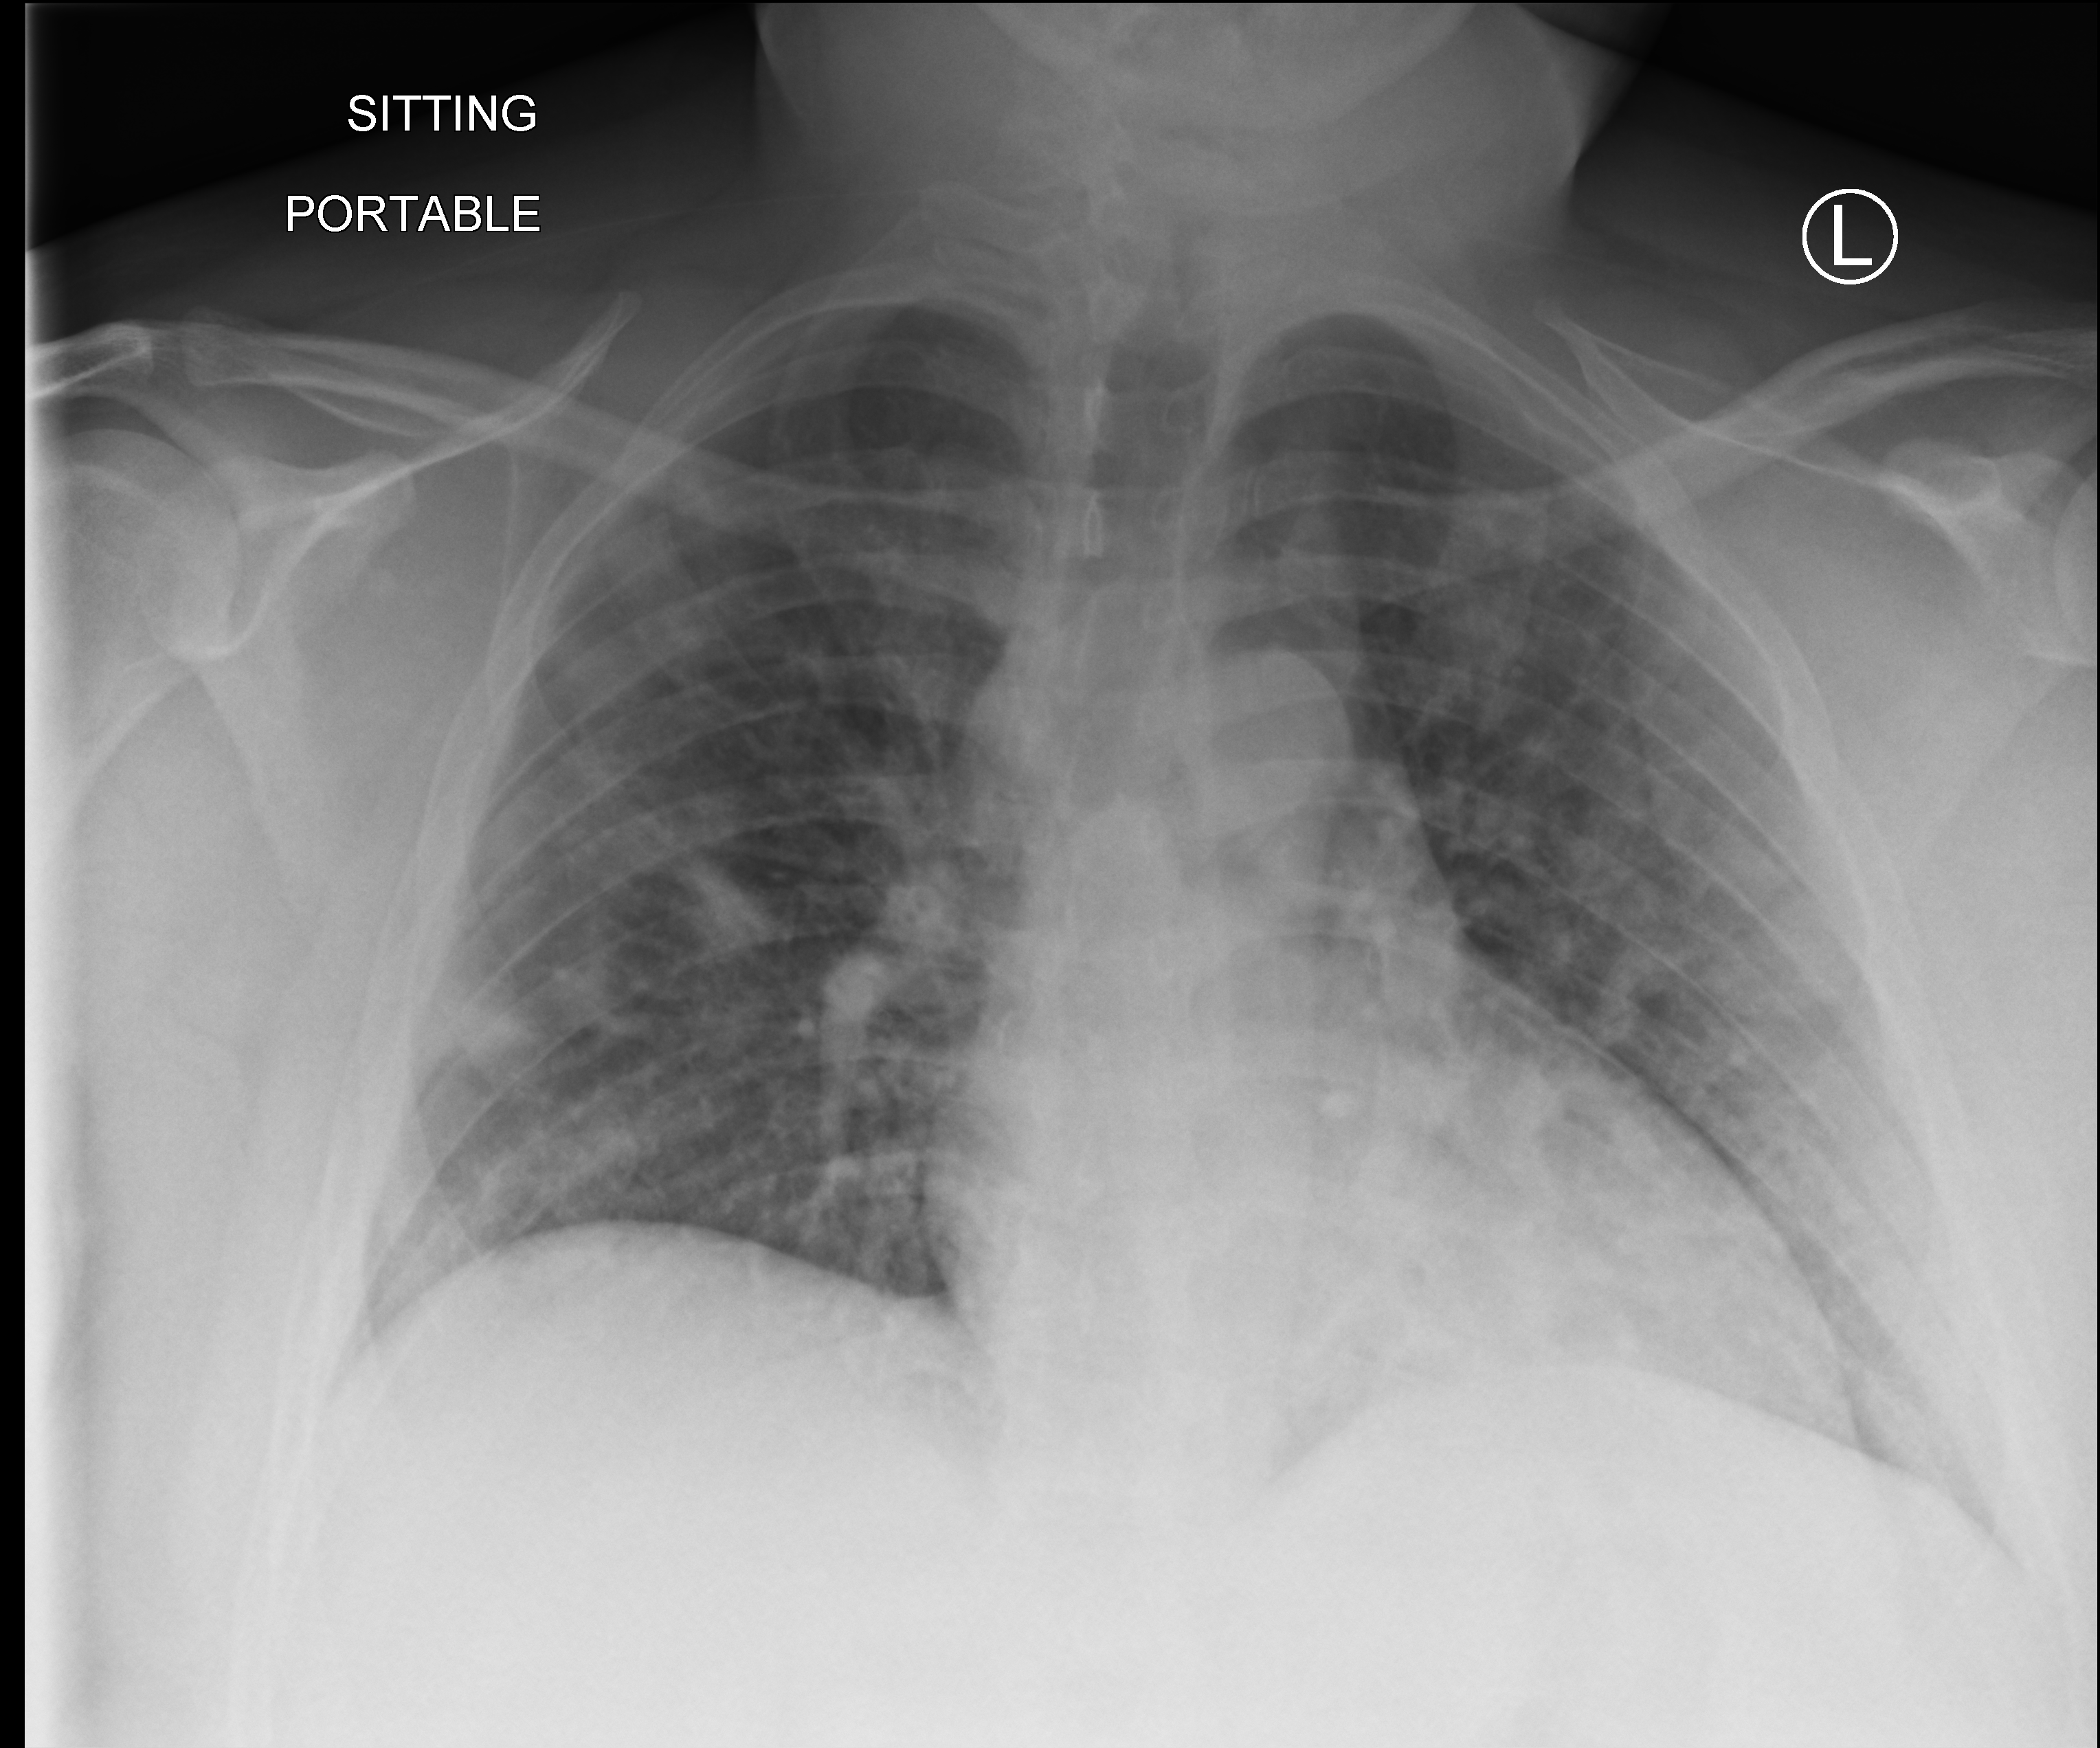
Portable chest radiograph; anteroposterior (AP) projection. Patient hospitalised with COVID-19; male, aged 18–59 years.
From the hospital-stay record, not from the radiograph (when in the stay this image was taken is not recorded): admitted to intensive care during this hospital stay: no.